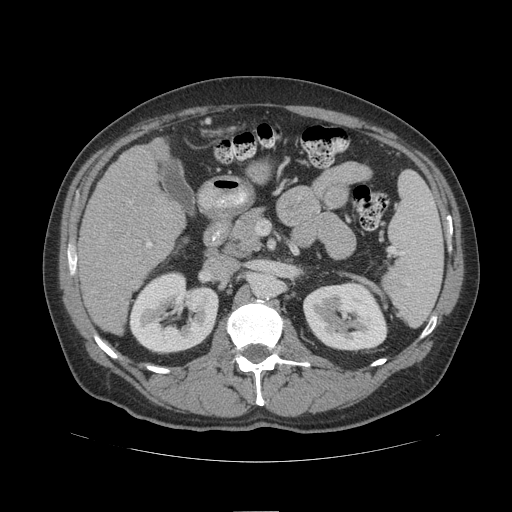
Contrast-enhanced abdominal CT (liver protocol), one axial slice. Slice 52 of 109 in the series (ordered by position). 140 kVp. Soft-tissue window (W 400 / L 40 HU). 2.5 mm slice thickness. 512 × 512 image matrix, field of view 420 × 420 mm. Case-level facts recorded for this patient, not image findings: diagnosis: hepatocellular carcinoma (patient treated with transarterial chemoembolisation; whether this scan precedes or follows treatment is not stated here); TNM stage (as recorded): Stage-IIIB; Child-Pugh class: A; tumour differentiation: poorly differentiated; tumour nodularity: multinodular.
Annotated regions visible in this slice (semi-automatically segmented with operator editing):
- liver parenchyma outside the tumour (the mass and vessels are separate outlines, so this box may not span the whole liver): box from (x=78, y=138) to (x=184, y=334) px
- liver vessels: (x=146, y=242)–(x=152, y=247)